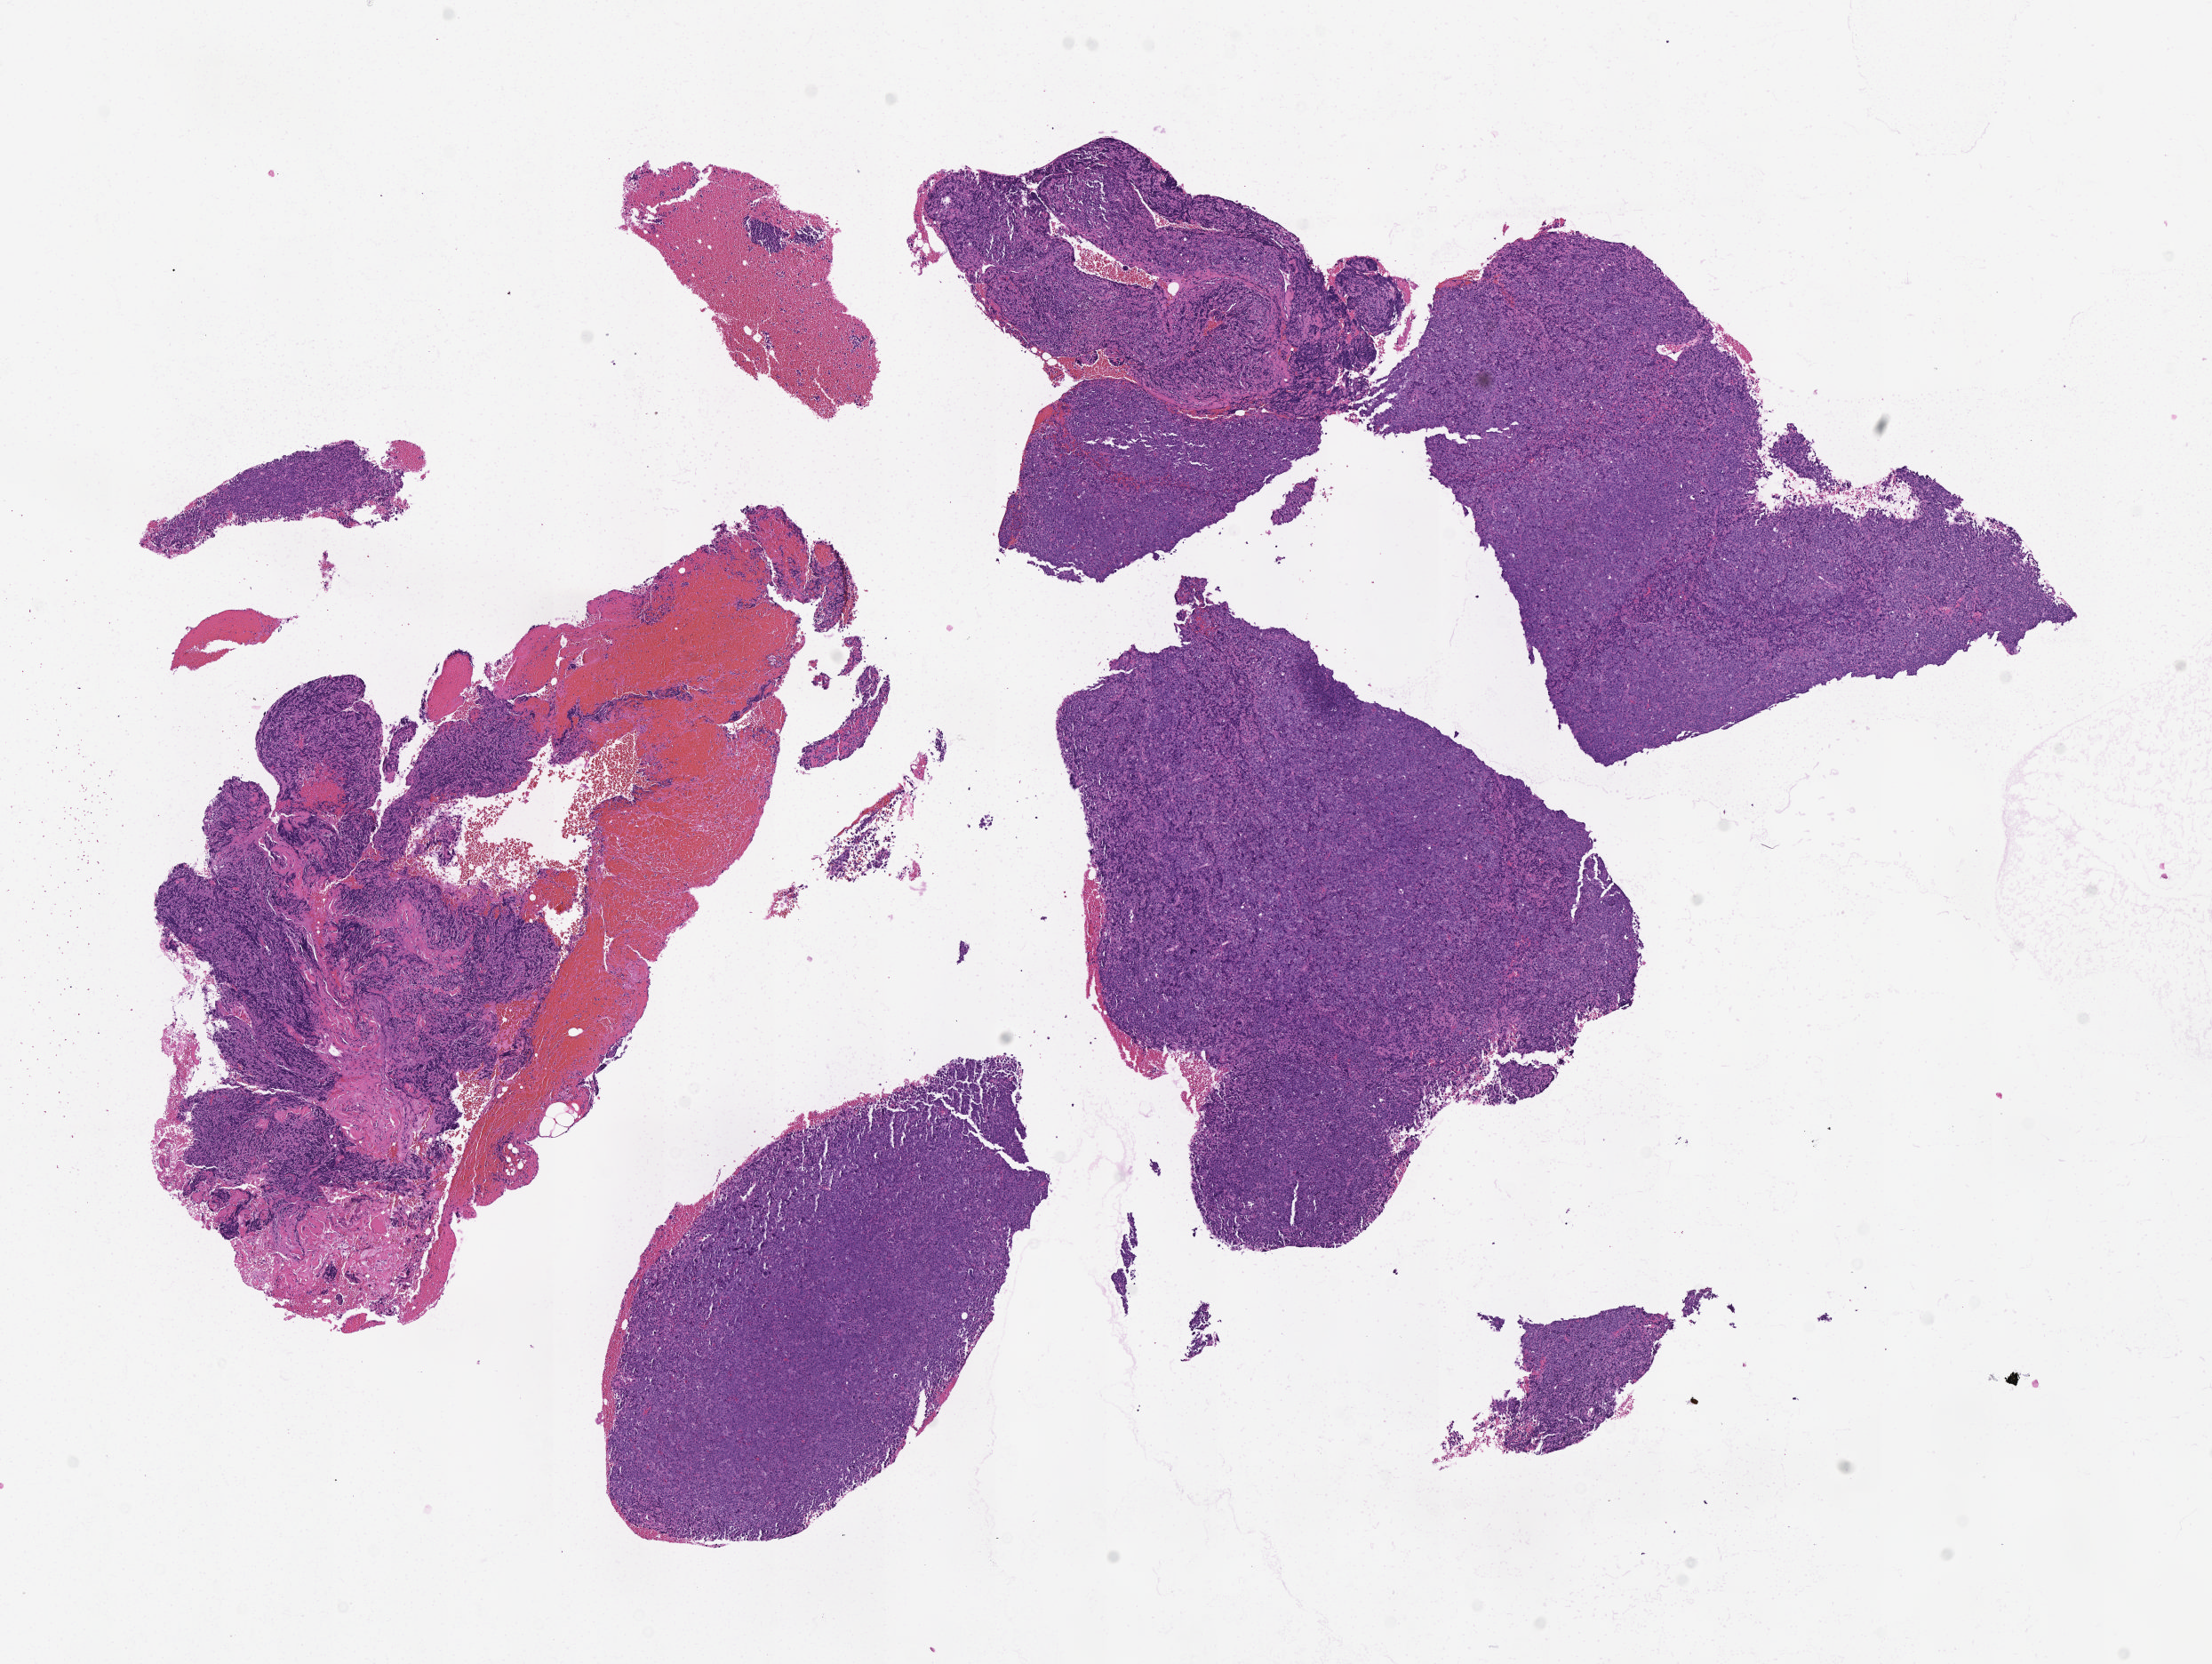
Digitized haematoxylin and eosin-stained section, whole scanned area (about 10.1 x 7.6 mm) shown as a low-resolution overview; specimen: tumor tissue; anatomic site: lymph node. Patient: female, aged 71.
• histologic diagnosis: Diffuse large B-cell lymphoma, NOS